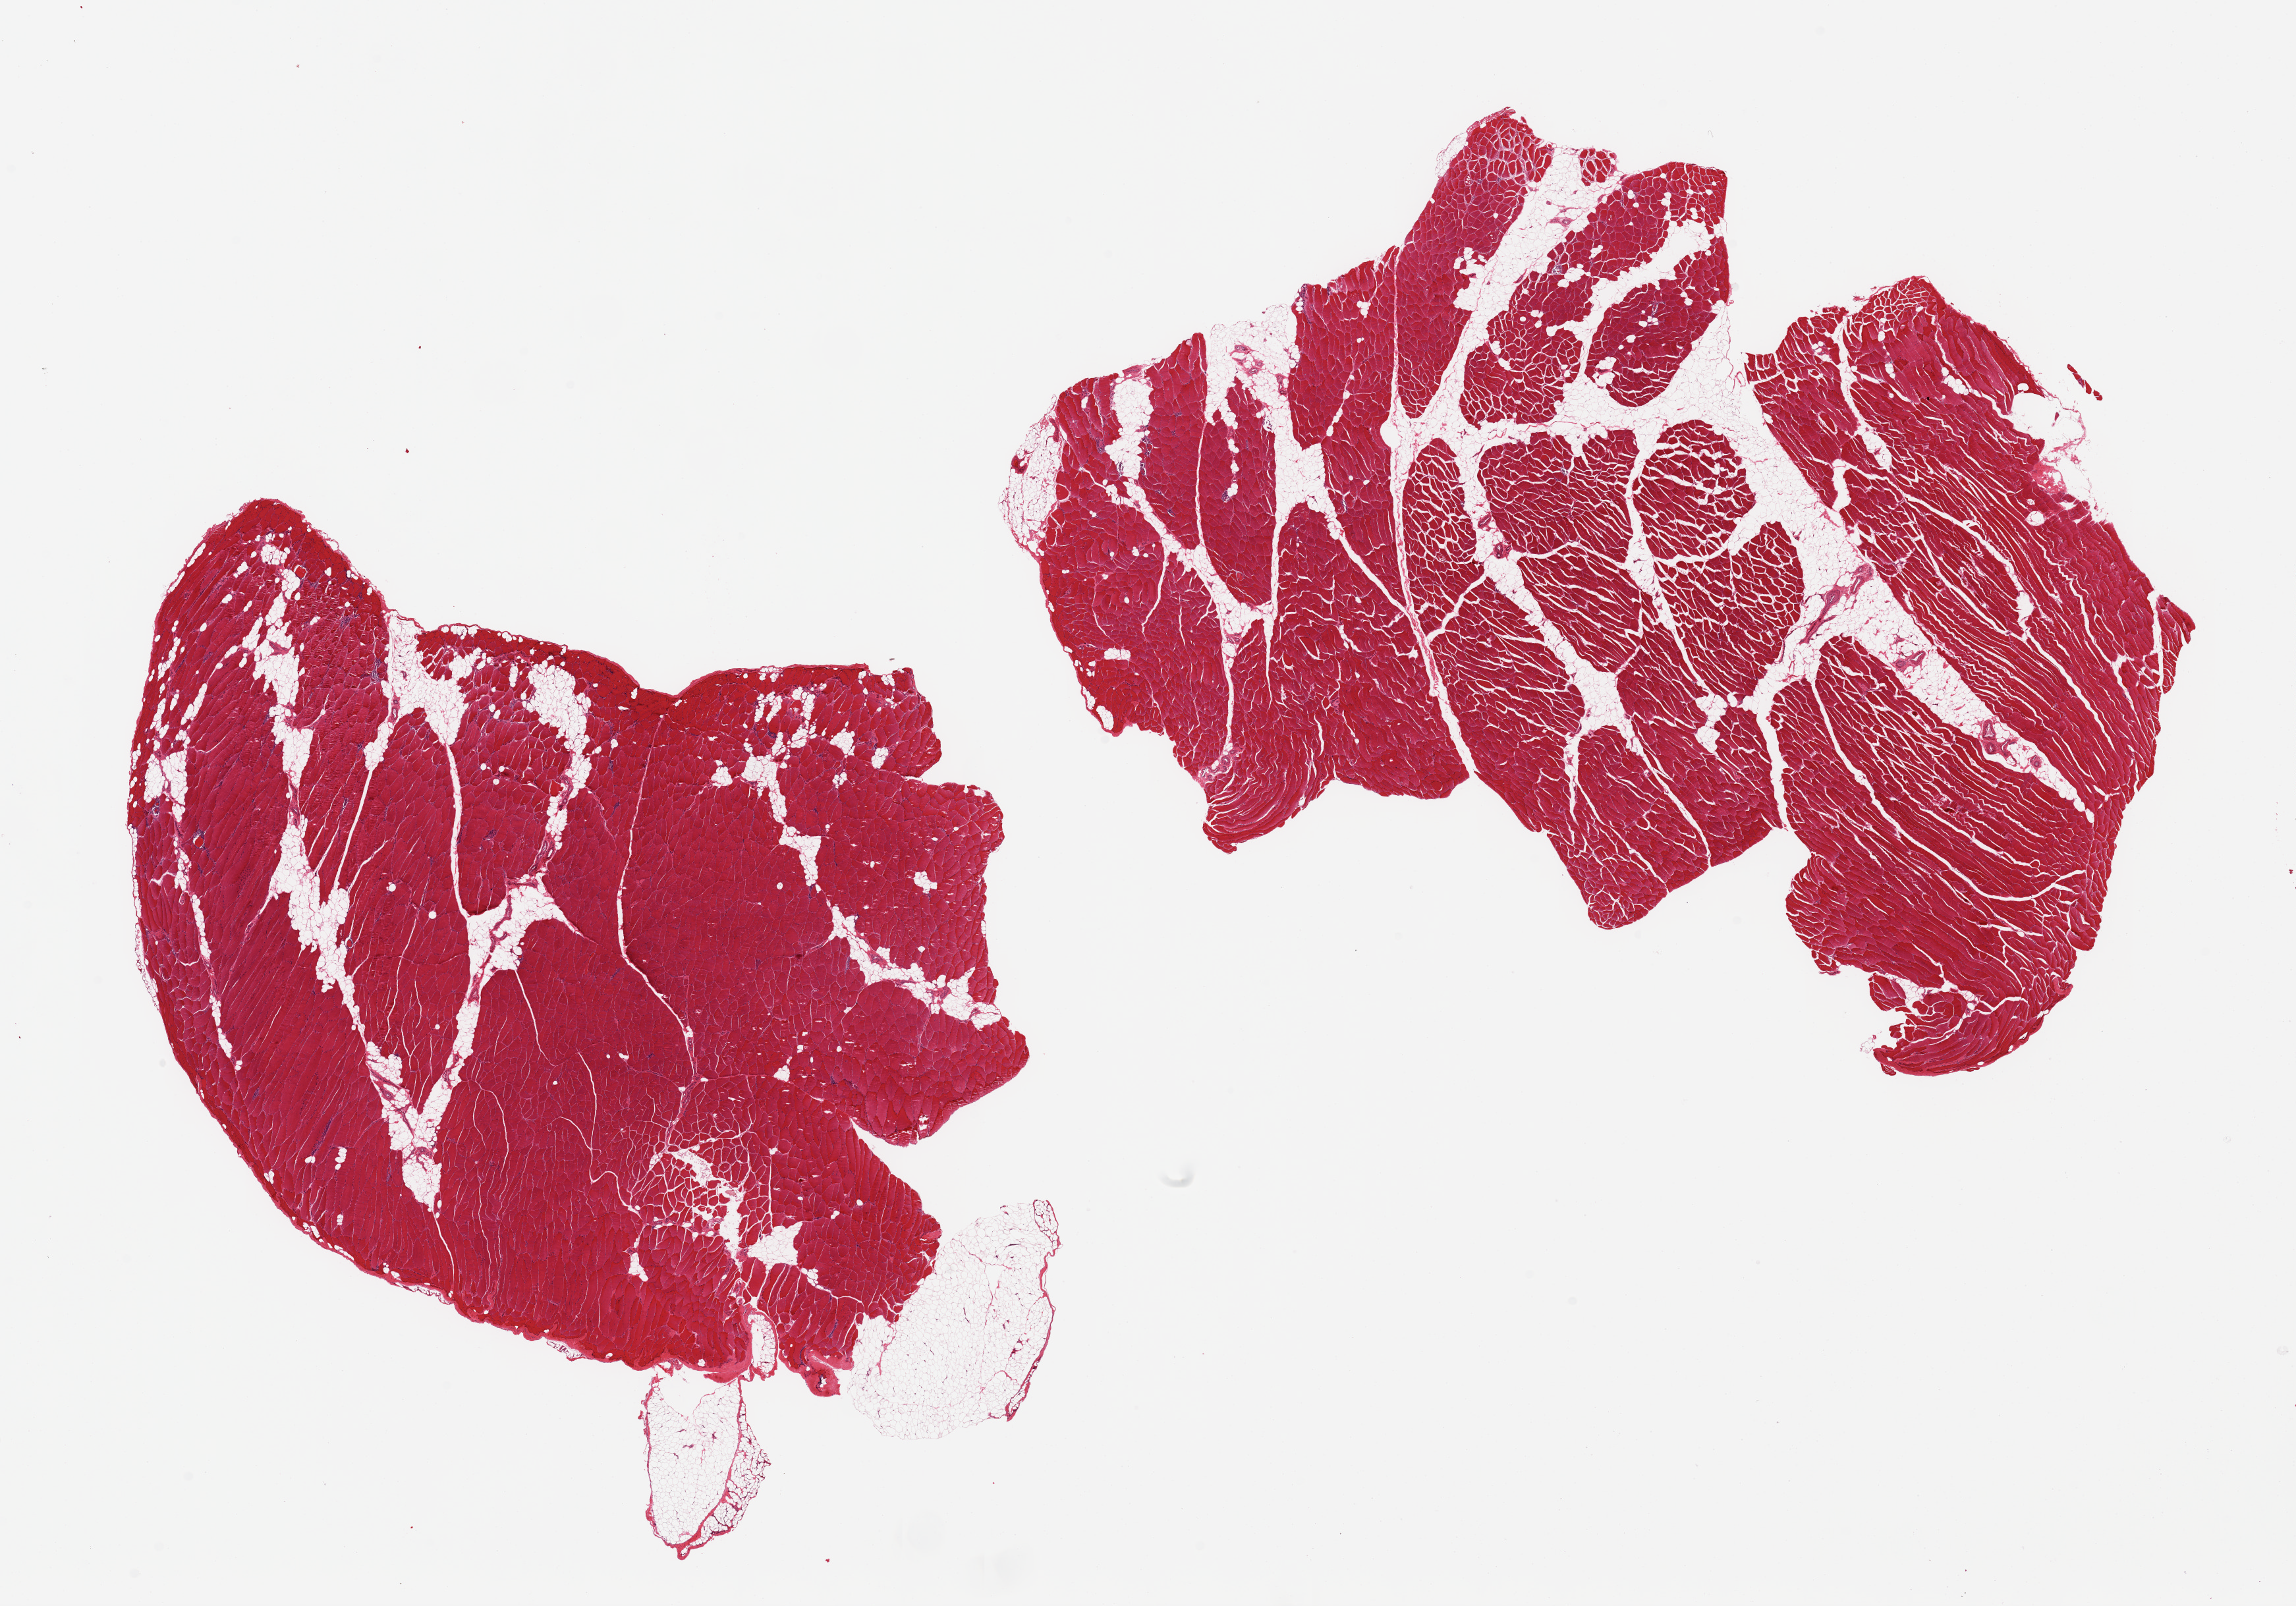
Digitized H&E-stained section, whole scanned area (about 27.6 x 19.3 mm) shown as a low-resolution overview, PAXgene-fixed paraffin-embedded (PFPE) section, section of skeletal muscle (target tissue), tissue donor sample. Male donor.
Reviewer comment on this tissue sample: 2 pieces; 10% internal fat.